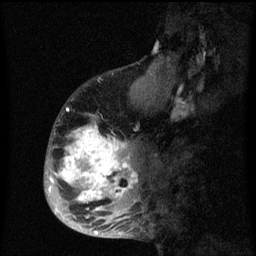
Breast MRI (dynamic contrast-enhanced), one sagittal slice; position 23 of 60 along the scan axis; dynamic contrast-enhanced series, image 2 of 3 at this slice position (ordered by acquisition); 1.5 T; TE 4.2 ms, TR 8 ms; 2 mm slice thickness; 256 × 256 image matrix, field of view 190 × 190 mm. Female patient, age 50 years.
Outlined on this slice (semi-automatic segmentation, software-assisted and operator-edited):
- analysis volume of interest (the breast-tissue region the enhancement analysis was run in; not a lesion): bounding box (x1, y1, x2, y2) in pixels: (44, 90, 142, 216)
- tumour enhancement mask (voxels above the 70 % enhancement threshold inside the analysis volume of interest): (48, 124, 138, 216)